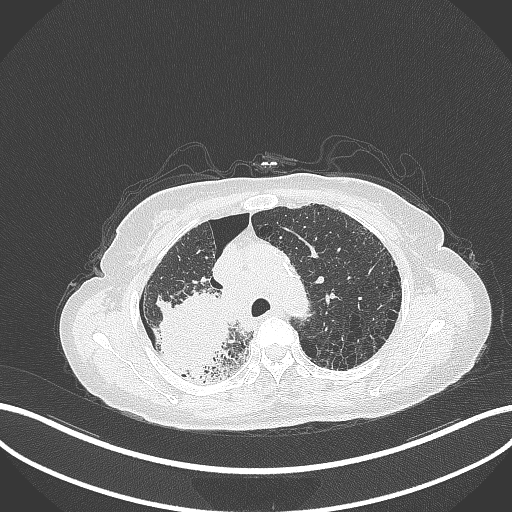
Chest CT, one axial slice; slice 256 of 408 in the series (ordered by position); reconstruction kernel B70f; 120 kVp; lung window (W 1500 / L -600 HU); 1 mm slice thickness; 512 × 512 image matrix, field of view 400 × 400 mm. Female patient, age 64 years. Case-level facts recorded for this patient, not image findings: clinical TNM (as recorded): T3 N3 M0.
Annotated regions visible in this slice (bounding box drawn by a radiologist):
- lung tumour (recorded histology: squamous cell carcinoma): bounding box (x1, y1, x2, y2) in pixels: (149, 288, 233, 382)